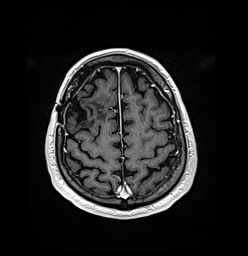
Brain MRI from a brain-tumour surgery series, one axial slice; position 38 of 176 along the scan axis; T1-weighted post-contrast; 248 × 256 image matrix, field of view 242 × 250 mm. From the clinical record (not read from this slice): histopathology: Oligodendroglioma; WHO grade: 3; IDH mutation: yes; tumour location: Right Frontal.
Outlined on this slice (manually delineated by an expert):
- previous resection cavity: bounding box [x1, y1, x2, y2] px = [68, 94, 88, 124]